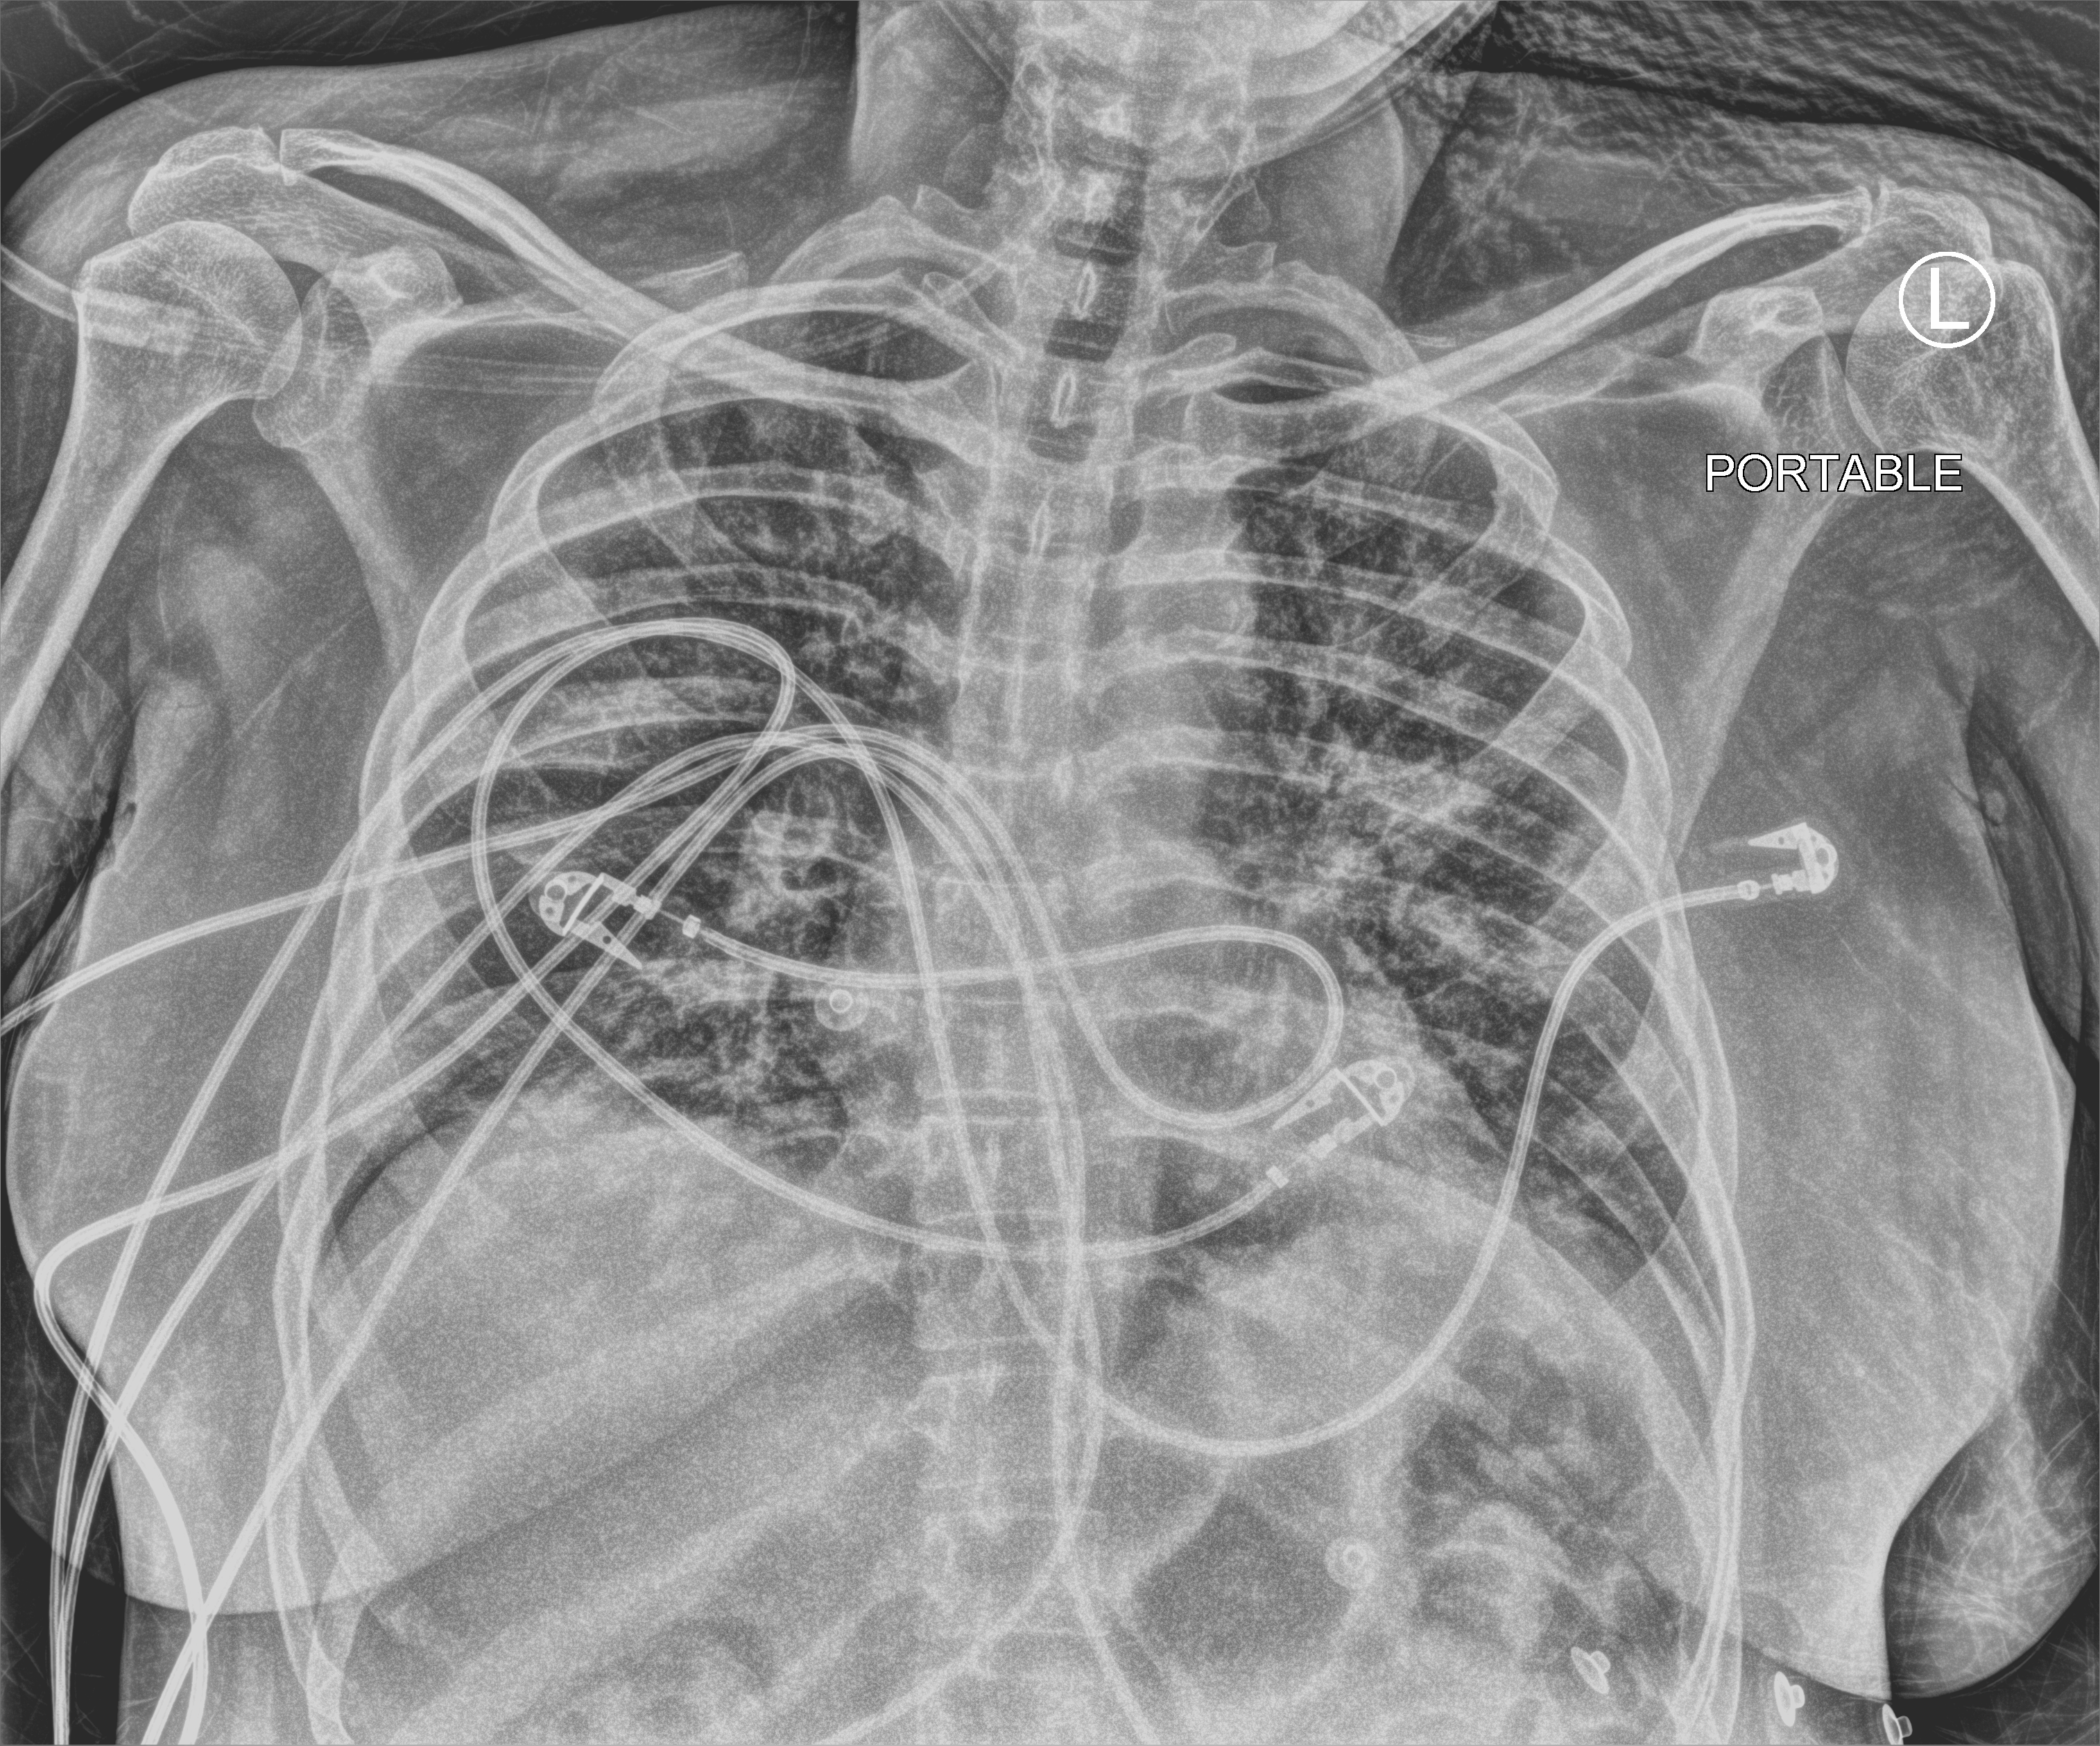
Bedside chest radiograph (computed radiography), anteroposterior (AP) projection. Adult patient hospitalised with COVID-19, age 18–59 years.
Hospital-stay facts (about this admission, not read from this image; timing relative to this image not recorded): mechanically ventilated during this hospital stay: yes.